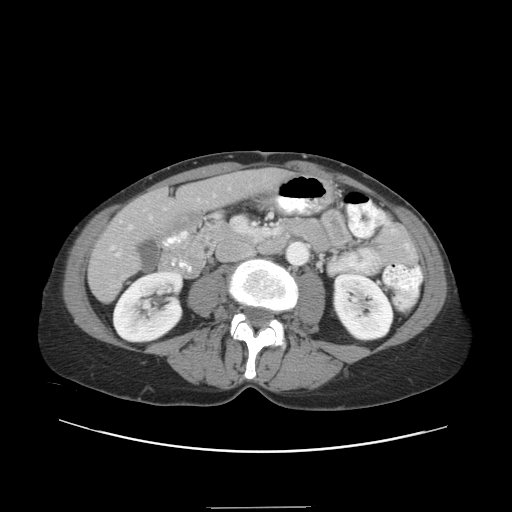
Contrast-enhanced abdominal CT, one axial slice; position 10 of 38 along the scan axis; reconstruction kernel STANDARD; intravenous contrast given; soft-tissue window (W 400 / L 40 HU); 512 × 512 image matrix, field of view 388 × 388 mm. Female patient, age 64 years. From the clinical record (not read from this slice): diagnosis: colorectal cancer liver metastases, imaged before liver resection; multiple liver metastases: no; largest metastasis: 3.8 cm; disease in both lobes: yes.
Annotated regions visible in this slice (expert manual segmentation):
- hepatic veins: bounding box <110,194,216,250> (left, top, right, bottom; pixels)
- liver: <90,170,284,300>
- planned liver remnant (the part of the liver to remain after resection): <166,170,285,216>
- portal vein (with intrahepatic branches): <116,188,230,257>